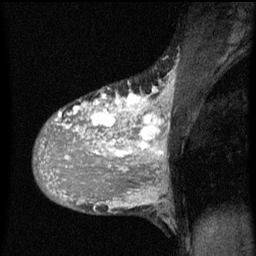
Breast MRI (dynamic contrast-enhanced), one sagittal slice; dynamic contrast-enhanced series, image 2 of 3 at this slice position (ordered by acquisition); 1.5 T; TE 4.2 ms, TR 8 ms; 2 mm slice thickness; 256 × 256 image matrix, field of view 180 × 180 mm. Patient: female, 36 years.
Annotated regions visible in this slice (semi-automatically segmented with operator editing):
- analysis volume of interest (the breast-tissue region the enhancement analysis was run in; not a lesion): bounding box <36,82,167,161> (left, top, right, bottom; pixels)
- tumour enhancement mask (voxels above the 70 % enhancement threshold inside the analysis volume of interest): <40,88,167,161>